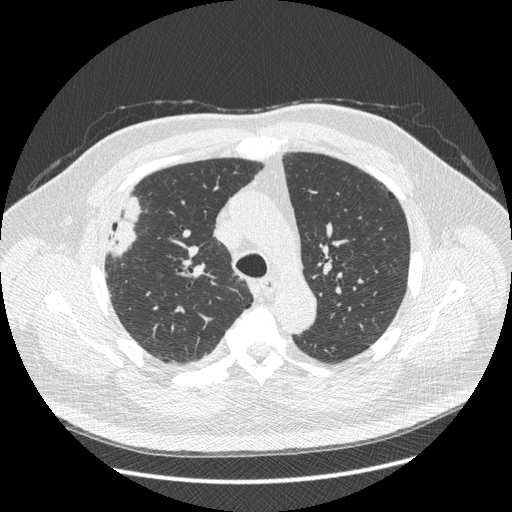
Low-dose screening chest CT, one axial slice; slice 301 of 426 in the series (ordered by position); reconstruction kernel STANDARD; lung window (W 1500 / L -600 HU); 1.25 mm slice thickness; 512 × 512 image matrix, field of view 400 × 400 mm.
Outlined on this slice (manually delineated by an expert):
- lesion 1 (tumor, upper lobe of right lung): box from (x=107, y=197) to (x=140, y=255) px